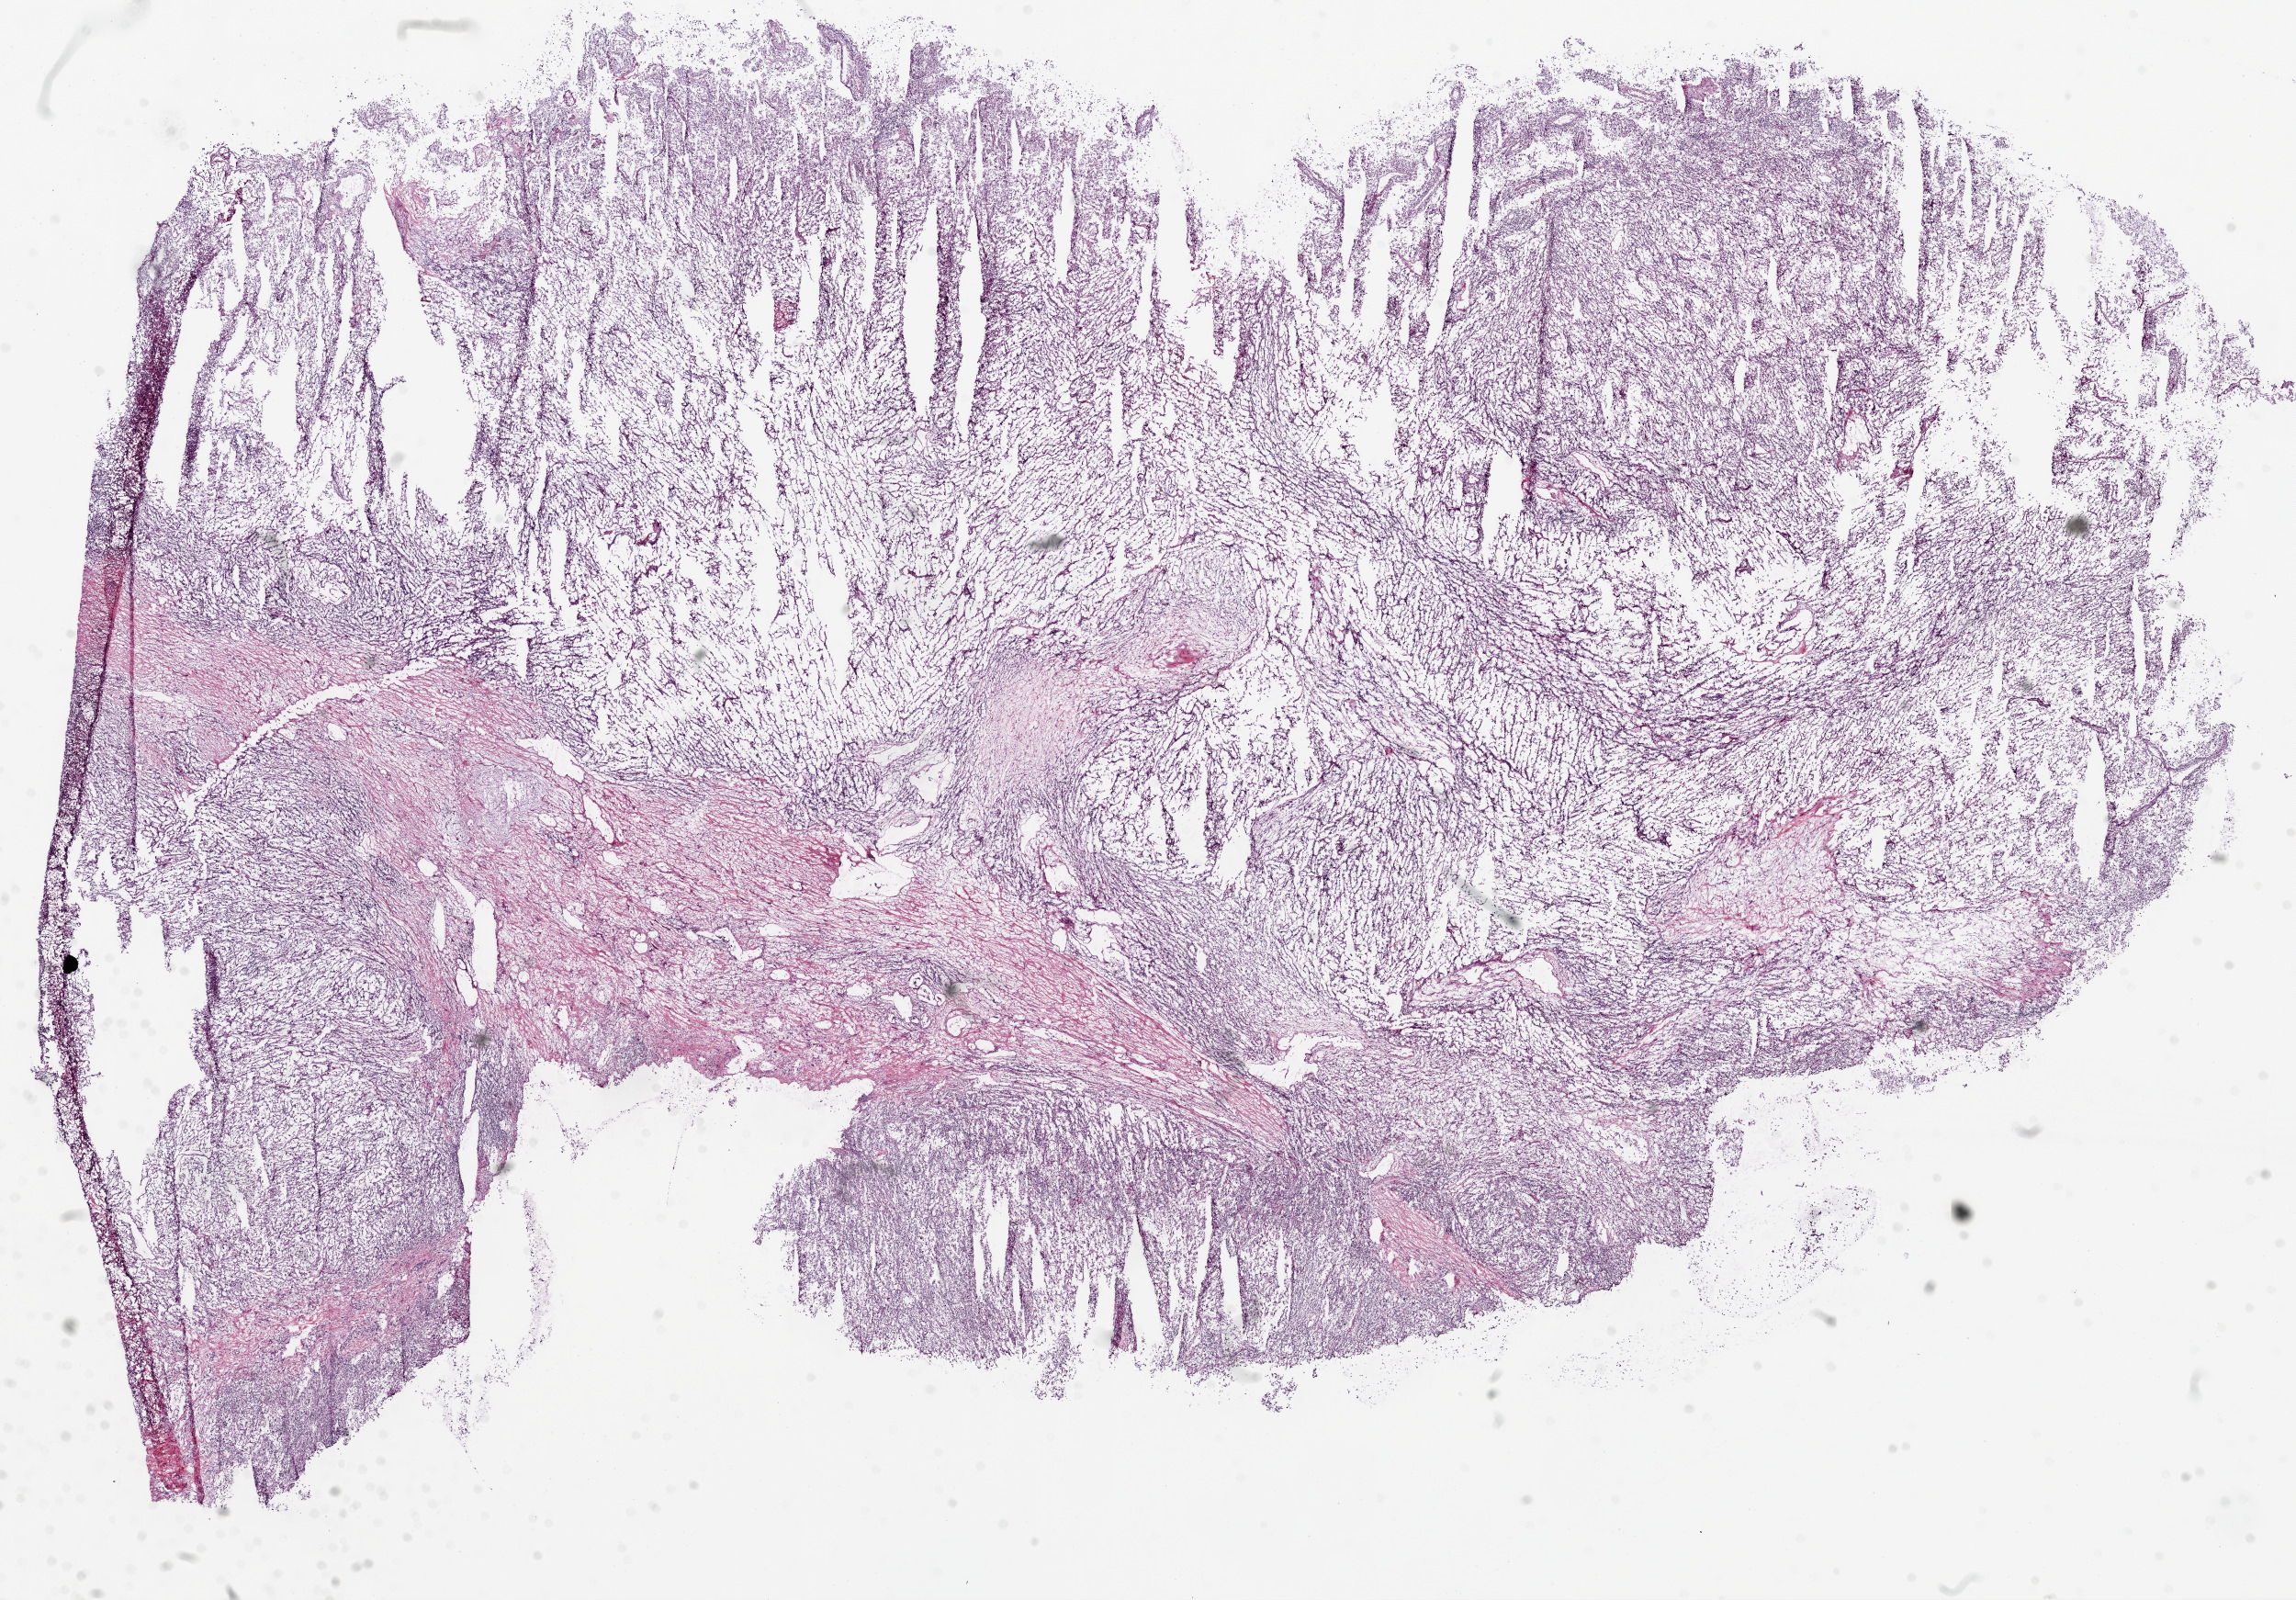
Whole-slide histology image, H&E — a low-resolution overview of the entire scanned area, about 20.1 x 14.0 mm (slide scanned at 20x); frozen section from the top of the tissue portion; primary tumour sample from the kidney. Female patient; age at initial diagnosis 46 years. Histologic grade: G4 (undifferentiated). Slide review estimates, as recorded: tumour cells 85%, tumour nuclei 80%, normal cells 0%, stromal cells 15%, necrosis 0%.
* AJCC pathologic stage: IV
* diagnosis: Clear cell adenocarcinoma, NOS